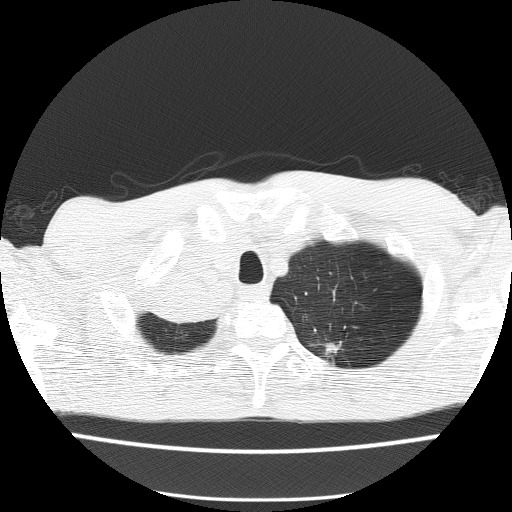
Low-dose screening chest CT, one axial slice. Slice 130 of 150 in the series (ordered by position). Reconstruction kernel FC51. 120 kVp. Lung window (W 1500 / L -600 HU). 2 mm slice thickness. 512 × 512 image matrix.
Annotated regions visible in this slice (manually delineated by an expert):
- lesion 1 (tumor, hilum of right lung): bounding box <151,276,217,323> (left, top, right, bottom; pixels)